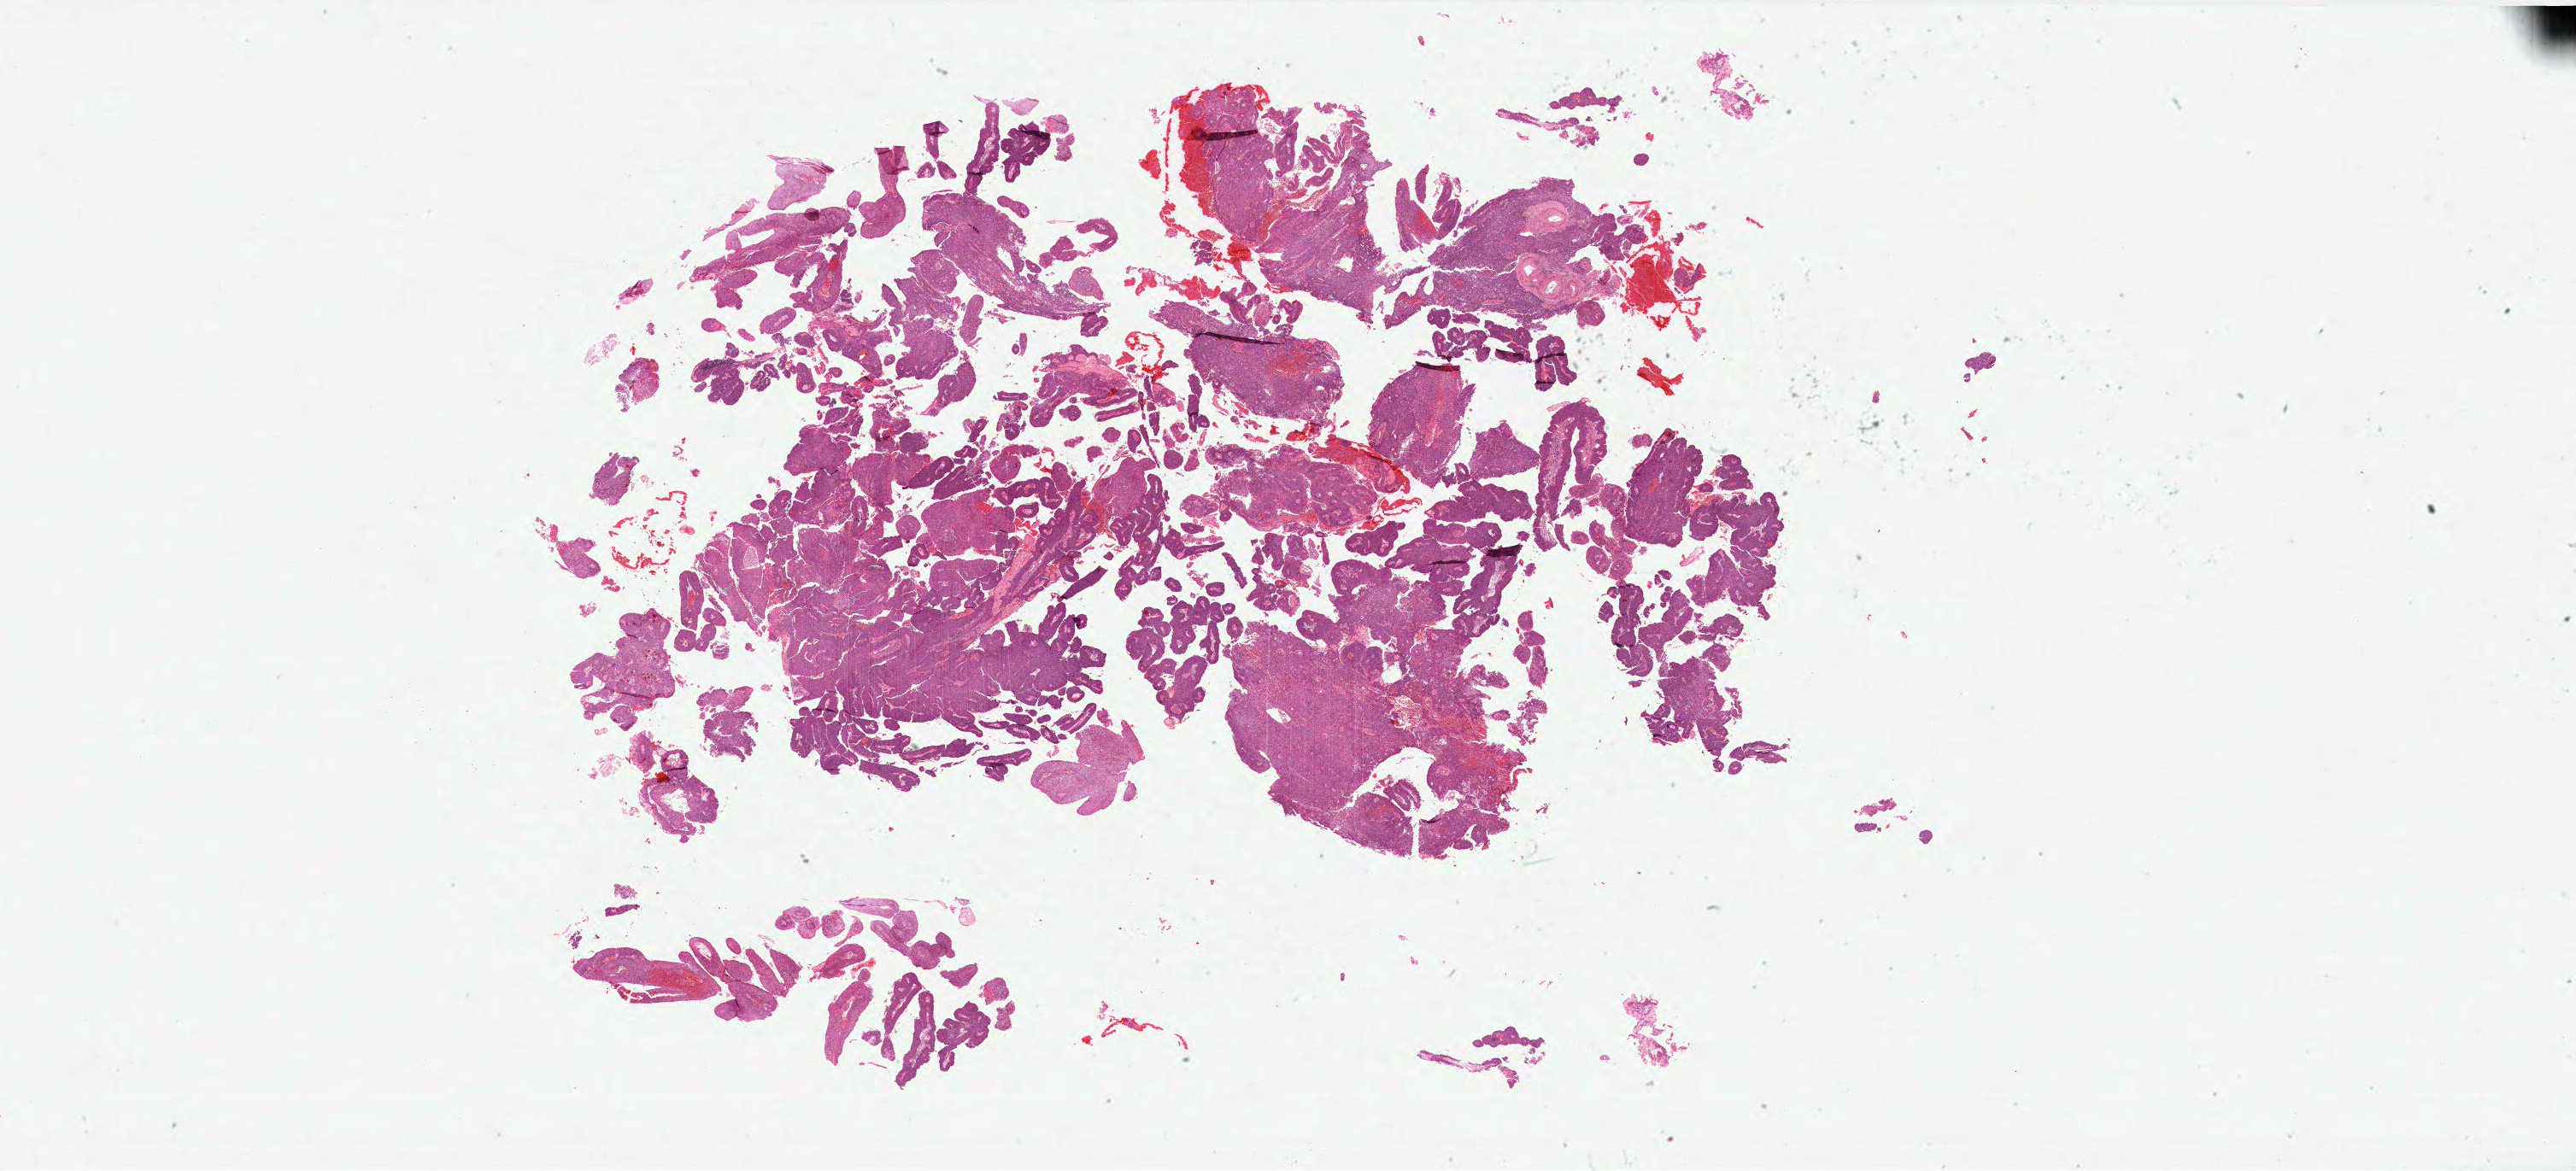
Whole-slide histology image, Hematoxylin and eosin (H&E) stained, shown as a low-resolution overview of the whole scanned area (about 48.3 x 21.9 mm, acquisition: 40x scan). Formalin-fixed paraffin-embedded (FFPE) diagnostic section. Cervix, primary tumour sample. Patient: female, age at initial diagnosis 63 years.
Pathologic diagnosis: Squamous cell carcinoma, NOS (cervix uteri).